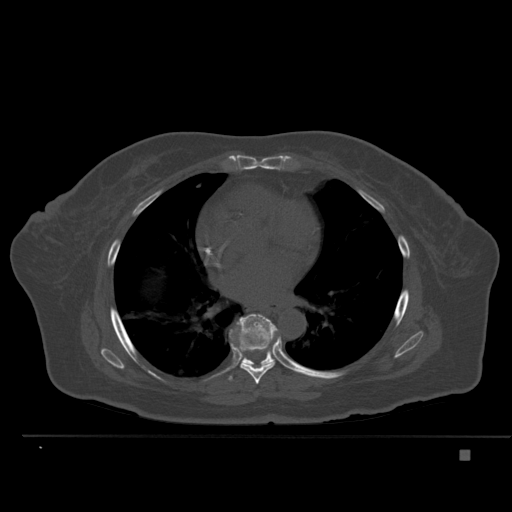
CT including the spine, one axial slice. Bone window (W 1800 / L 400 HU). 1.5 mm slice thickness. 512 × 512 image matrix. Female patient, age 74 years. Case-level facts recorded for this patient, not image findings: primary cancer: colon.
Structures marked on this image (semi-automatic segmentation, software-assisted and operator-edited):
- T7 vertebra: box from (x=229, y=327) to (x=275, y=384) px
- T8 vertebra: (x=233, y=314)–(x=279, y=365)